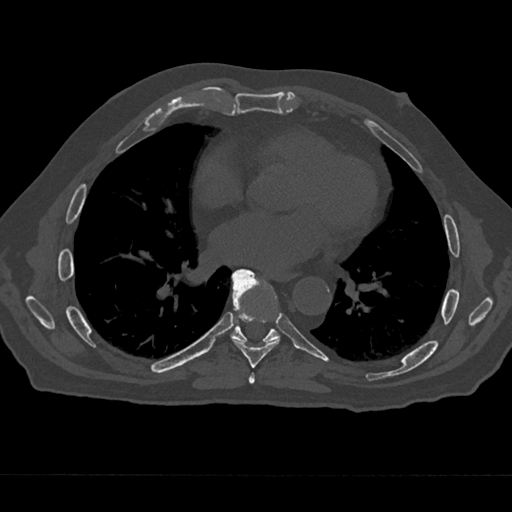
CT including the spine, one axial slice. Slice 348 of 797 in the series (ordered by position). Bone window (W 1800 / L 400 HU). 512 × 512 image matrix, field of view 377 × 377 mm. Patient: male, 75 years. From the clinical record (not read from this slice): primary cancer: renal.
Outlined on this slice (semi-automatically segmented with operator editing):
- T6 vertebra: box from (x=249, y=373) to (x=255, y=384) px
- T7 vertebra: (x=232, y=269)–(x=280, y=368)
- T8 vertebra: (x=230, y=272)–(x=280, y=343)